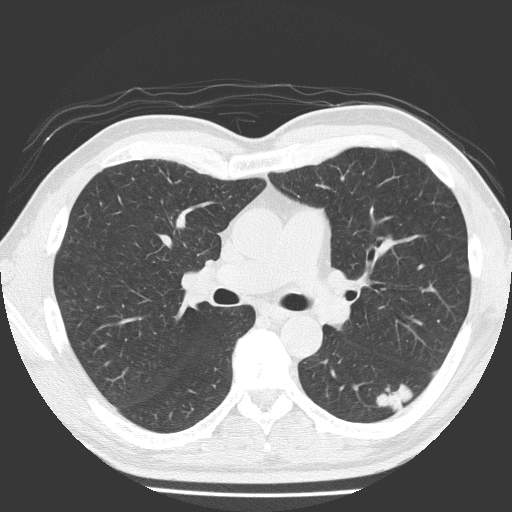
Axial slice from a low-dose chest CT screening exam. Baseline screening round. Lung window (W 1500 / L -600 HU). 2 mm slice thickness. Lung (sharp) reconstruction kernel (FC51). Male participant, aged 58 years at enrolment. Current smoker at enrolment.
Expert-annotated lung lesion, box from (x=368, y=374) to (x=425, y=423) px. The screening reader recorded 4 non-calcified nodules or masses ≥4 mm on this exam; which of them this box marks is not recorded. Later outcome: lung cancer diagnosed 99 days after this screen — adenosquamous carcinoma, left lower lobe, moderately differentiated (G2), stage IA (AJCC 6th edition), 28 mm at pathology.